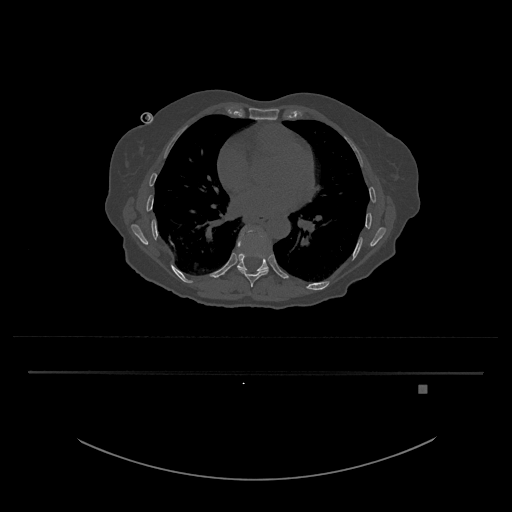
CT including the spine, one axial slice. Slice 741 of 797 in the series (ordered by position). Reconstruction kernel Br40s/3. 120 kVp. Bone window (W 1800 / L 400 HU). 0.5 mm slice thickness. 512 × 512 image matrix. Female patient, age 57 years. Case-level facts recorded for this patient, not image findings: primary cancer: cervical.
Annotated regions visible in this slice (semi-automatic segmentation, software-assisted and operator-edited):
- T10 vertebra: bounding box [x1, y1, x2, y2] px = [237, 226, 268, 272]
- T9 vertebra: [239, 269, 269, 288]